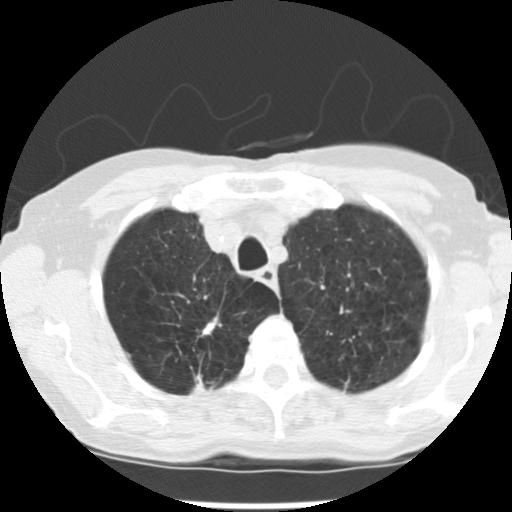
Axial slice from a low-dose chest CT screening exam; baseline annual screen; lung window (W 1500 / L -600 HU); 512 × 512 image matrix. Female, age 72 years at enrolment. Current smoker at enrolment.
2 expert-annotated lung lesions on this slice (largest first), bounding box [x1, y1, x2, y2] px = [181, 369, 228, 406]; [185, 310, 231, 347]. The screening reader recorded 3 non-calcified nodules or masses ≥4 mm on this exam (right upper lobe, left upper lobe, left lower lobe); which of them these boxes mark is not recorded. Lung cancer was diagnosed 50 days after this screen: adenocarcinoma, NOS, right upper lobe, moderately differentiated (G2), stage IB (AJCC 6th edition), 22 mm at pathology.